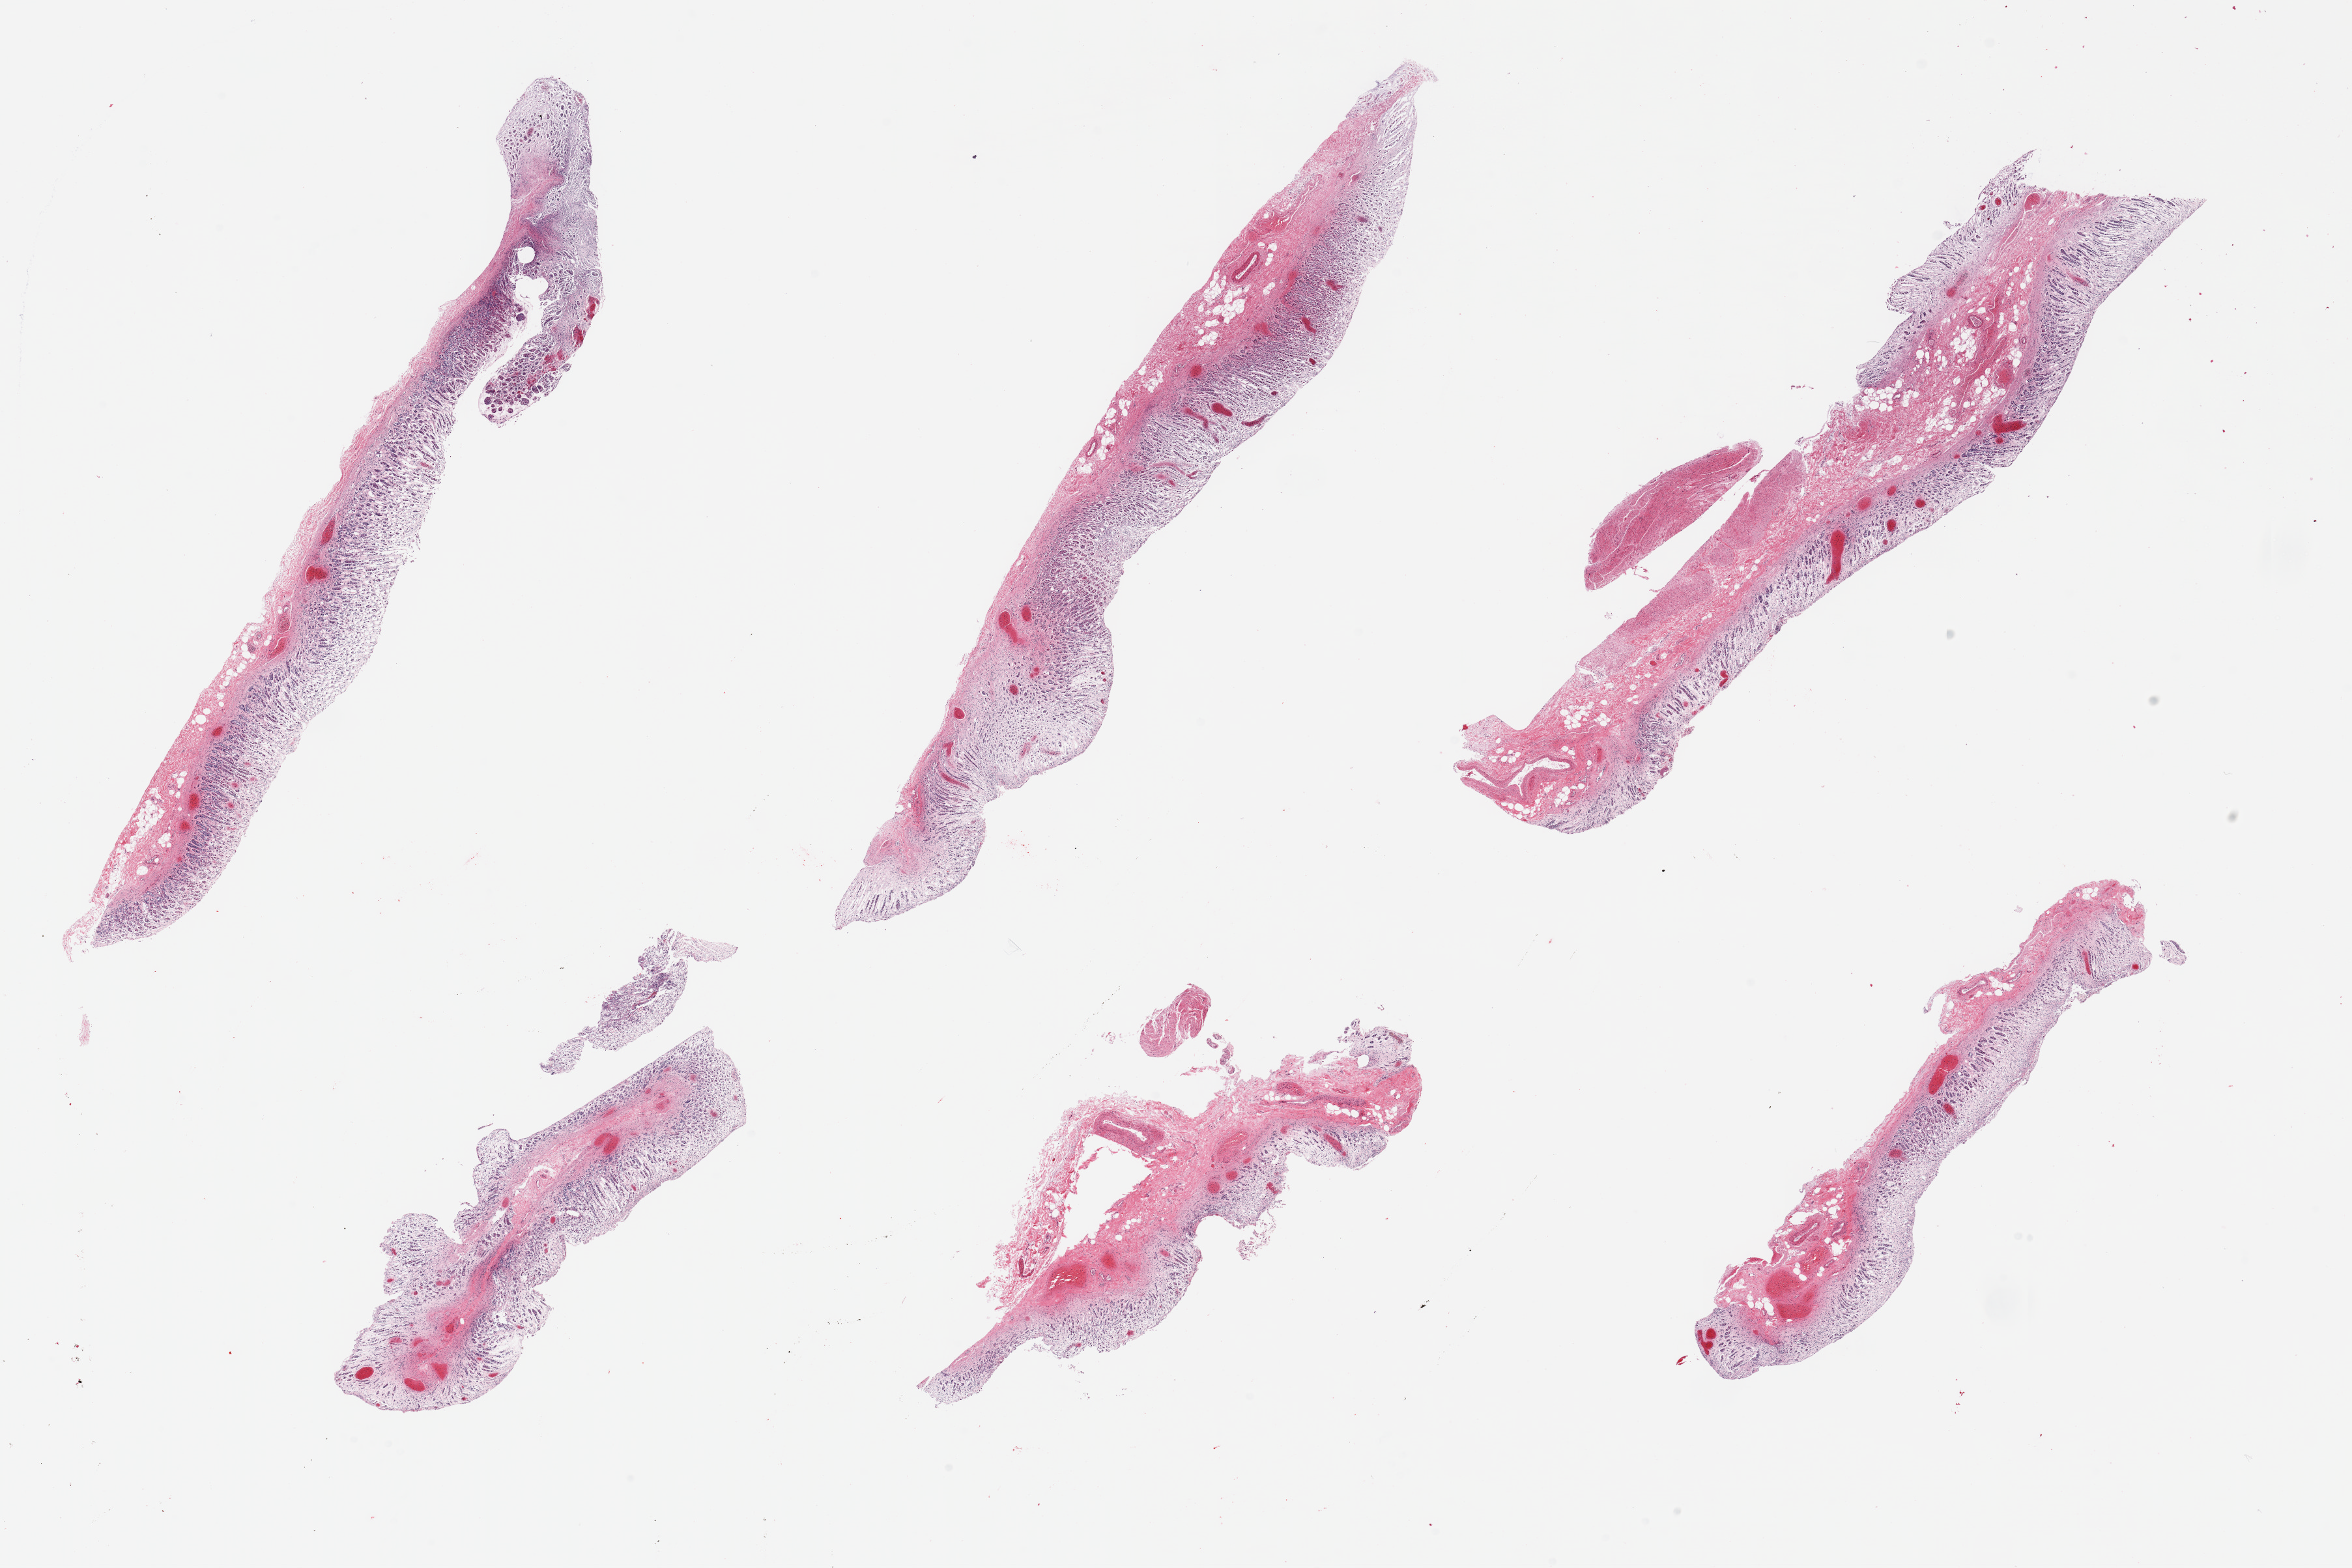
Digitized haematoxylin and eosin-stained section, brightfield, whole scanned area (about 28.5 x 19.0 mm) shown as a low-resolution overview. PAXgene-fixed paraffin-embedded (PFPE) section. Sampled site (target tissue): stomach. Donor tissue sample. Male donor.
Reviewer comment on this tissue sample: 6 pieces; autolyzed mucosa, minimal and partially autolyzed muscularis.